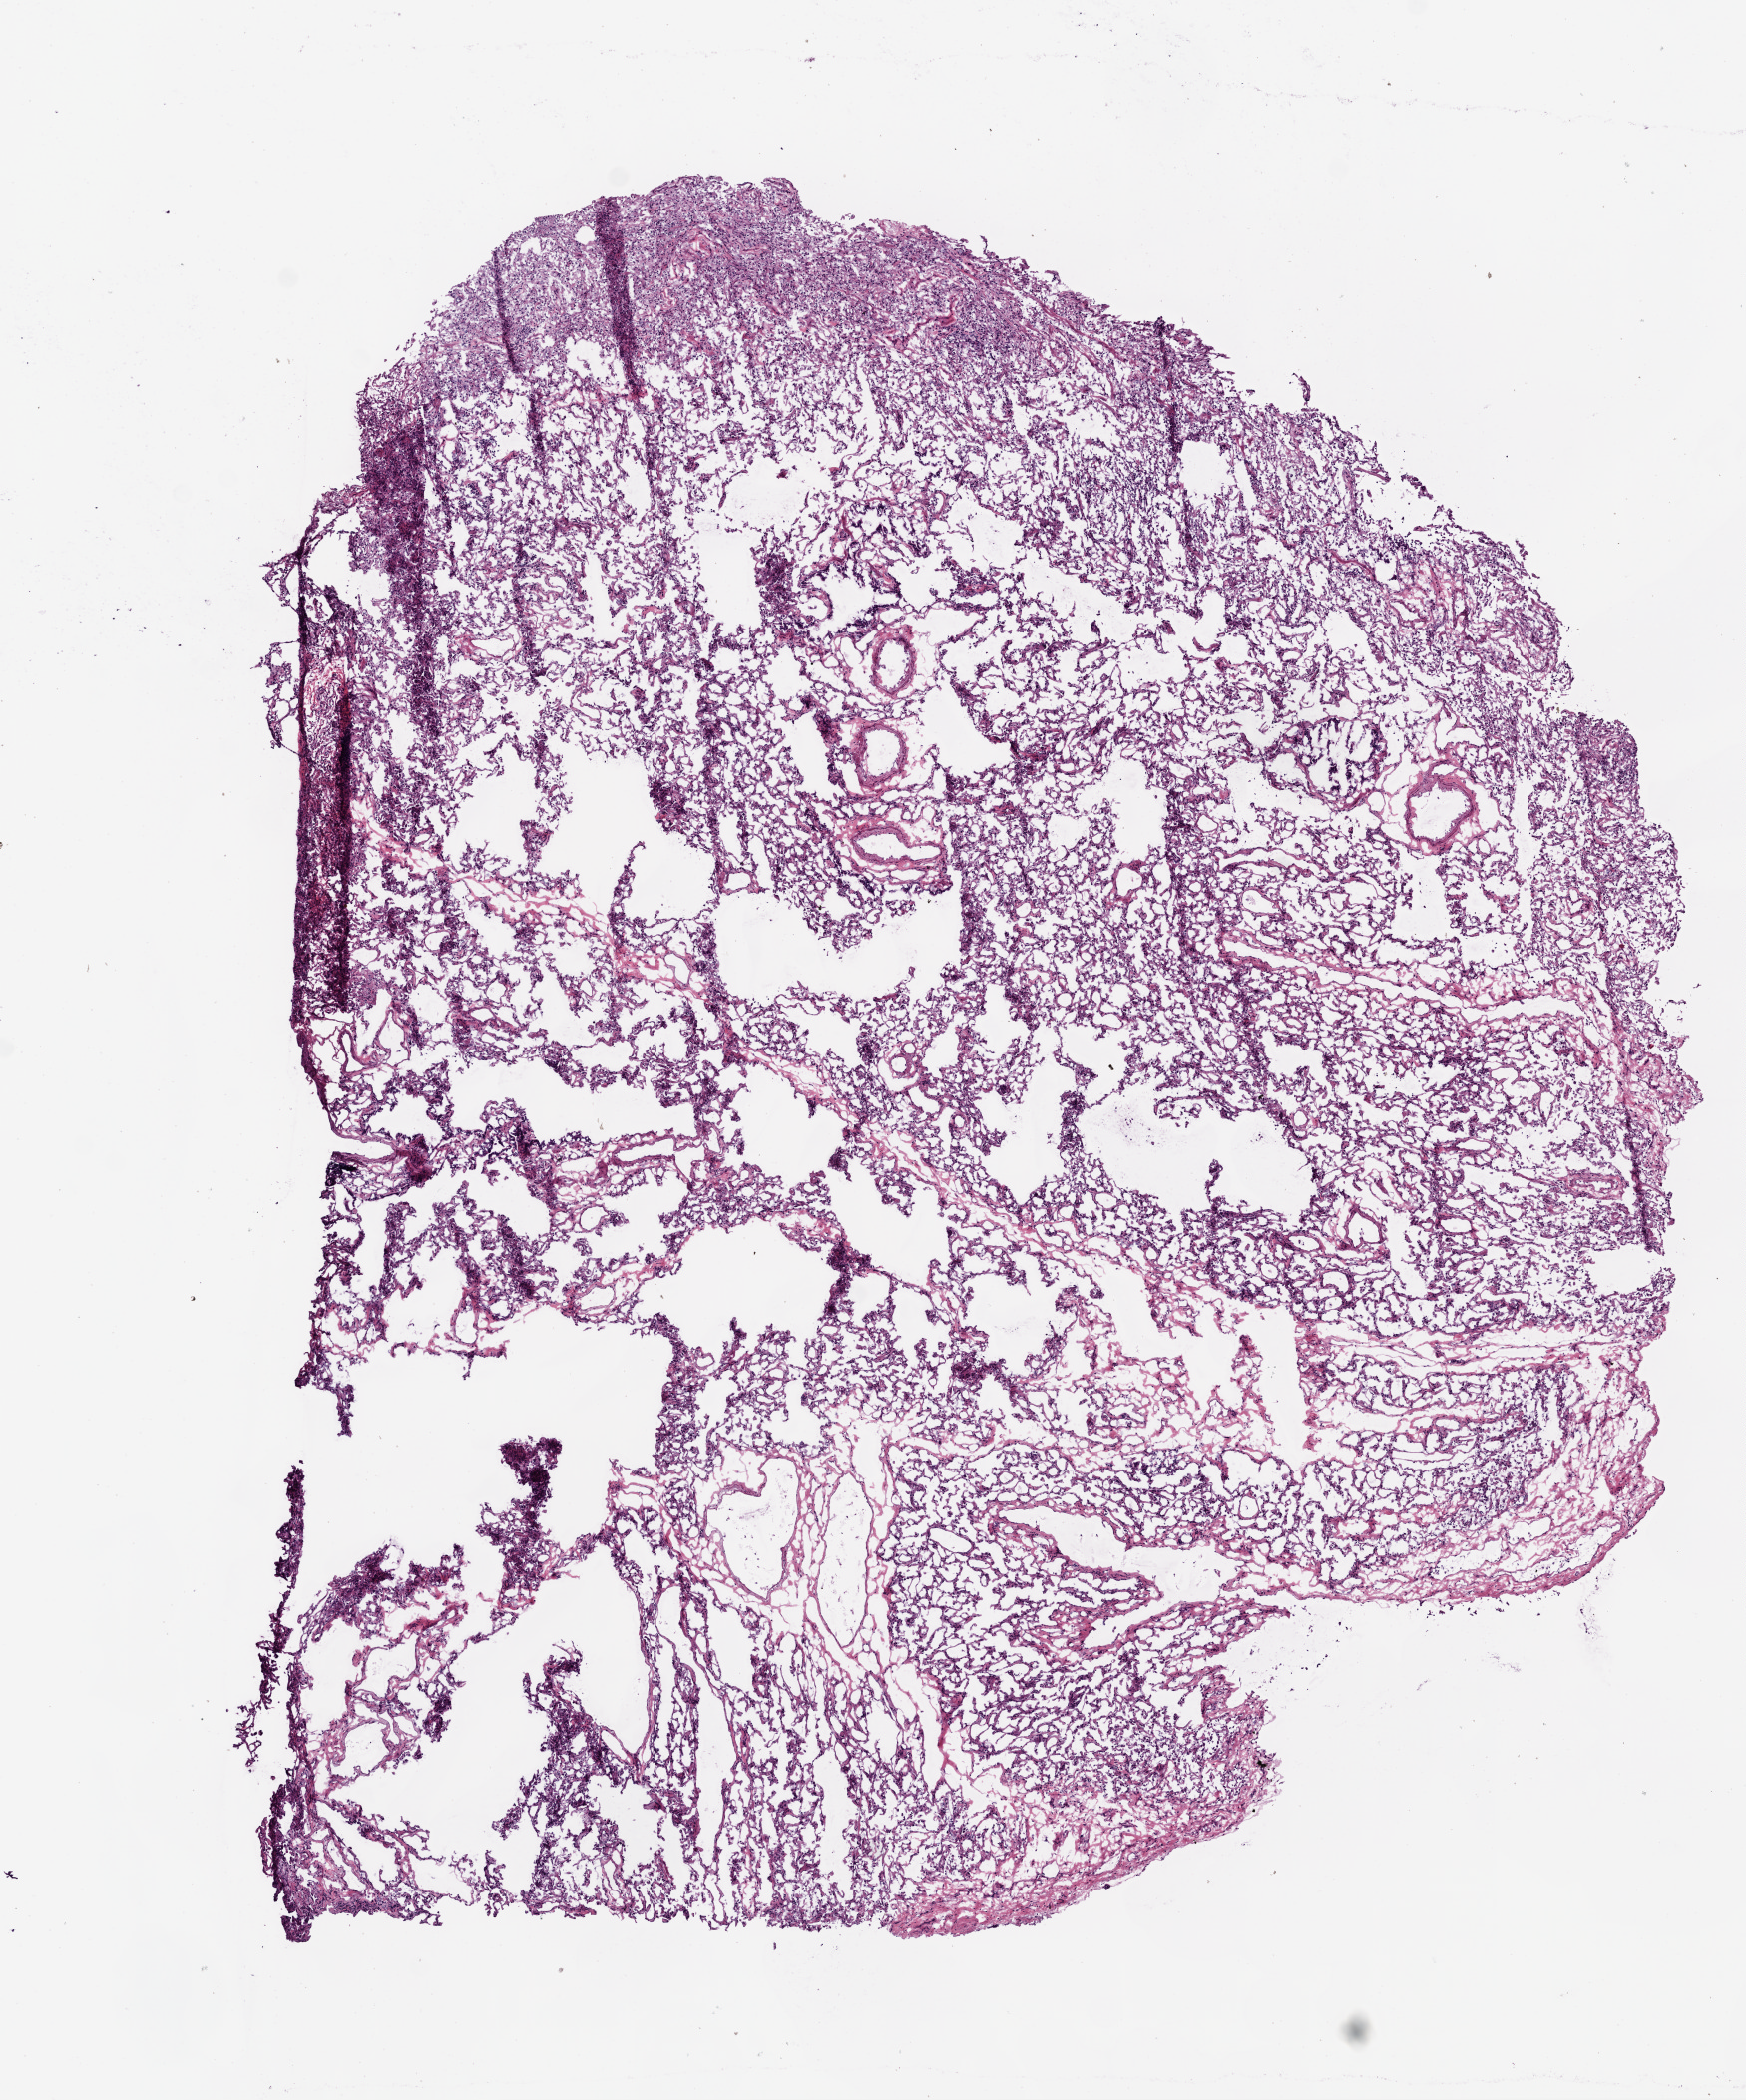
Whole-slide histology image, H&E — a low-resolution overview of the entire scanned area, about 7.0 x 8.4 mm (from a 20x scan); frozen section from the bottom of the tissue portion; sample: solid tissue normal (non-tumour tissue), lung. Patient: female, age at initial diagnosis 69 years.
This section: solid tissue normal (non-tumour) sample from the same patient. Patient diagnosis: Adenocarcinoma, NOS (middle lobe, lung).